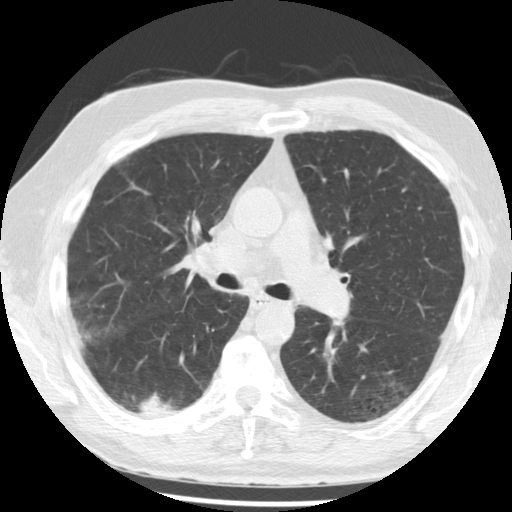
Axial slice from a low-dose chest CT screening exam, third annual screen, lung window (W 1500 / L -600 HU), 2.5 mm slice thickness, 120 kVp, slice 125 of 221 in the series. Male, age 68 years at enrolment.
Expert-annotated lung lesion, bounding box [x1, y1, x2, y2] px = [118, 378, 194, 433]. The screening reader recorded 3 non-calcified nodules or masses ≥4 mm on this exam (right lower lobe, right lower lobe, right lower lobe); which of them this box marks is not recorded. Official screen result: positive, other. Participant outcome: lung cancer diagnosed 48 days after this screen — squamous cell carcinoma, NOS, right lower lobe, moderately differentiated (G2), stage IB (AJCC 6th edition), 20 mm at pathology.